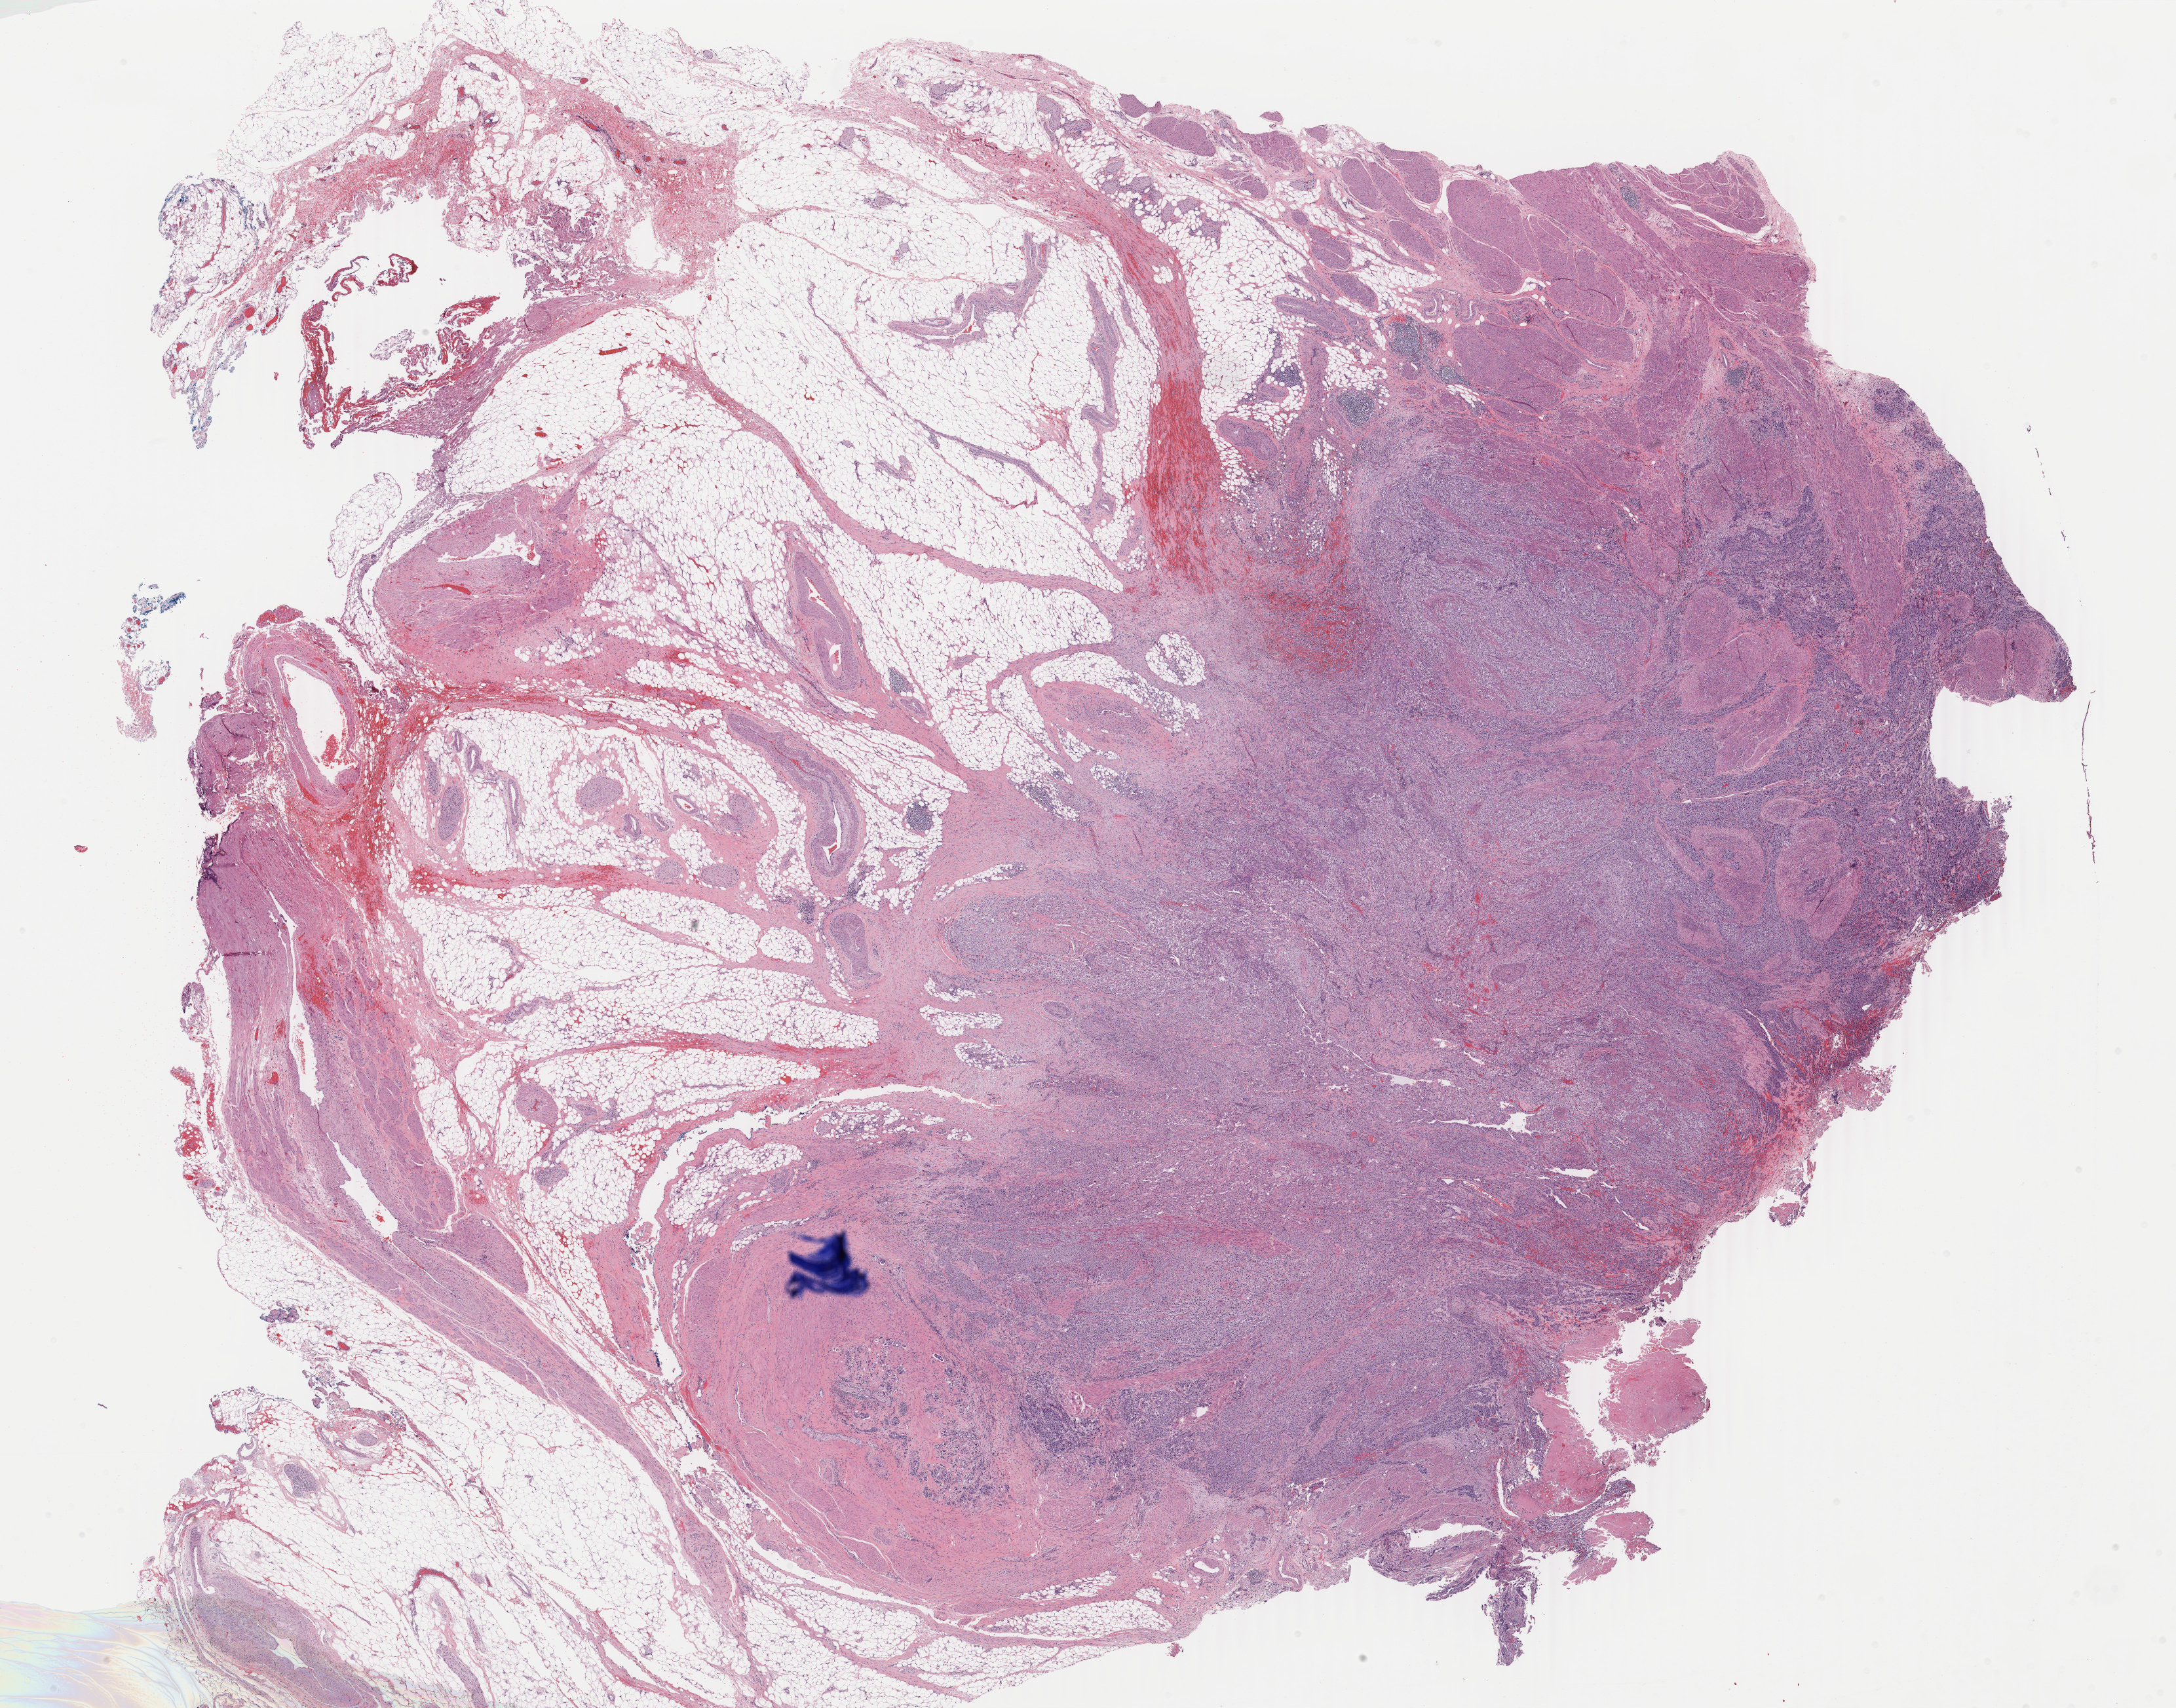
Hematoxylin and eosin (H&E) stained whole-slide image — low-resolution overview of the scanned area, about 26.4 x 20.7 mm. Formalin-fixed paraffin-embedded (FFPE) diagnostic section. Bladder, primary tumour sample. Male, age 62 years at initial diagnosis. Histologic grade: high grade.
- histologic diagnosis: Transitional cell carcinoma
- AJCC pathologic stage: IV (6th edition)
- lymph nodes positive (case pathology): 5 of 29 examined